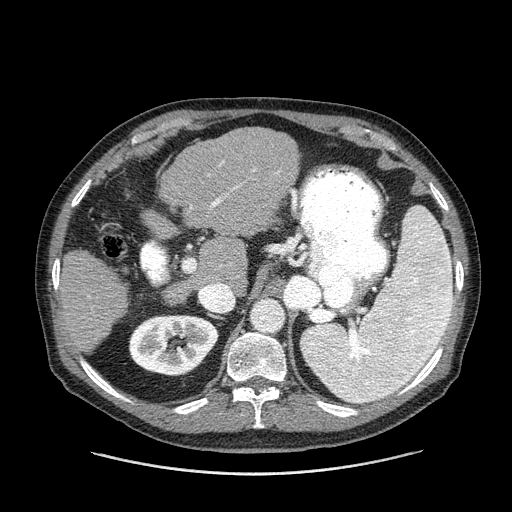
Contrast-enhanced abdominal CT (liver protocol), one axial slice; position 84 of 180 along the scan axis; reconstruction kernel STANDARD; 120 kVp; one of 2 acquisitions stored at this slice position; soft-tissue window (W 400 / L 40 HU); 2.5 mm slice thickness; 512 × 512 image matrix. From the clinical record (not read from this slice): diagnosis: hepatocellular carcinoma (patient treated with transarterial chemoembolisation; whether this scan precedes or follows treatment is not stated here); TNM stage (as recorded): Stage-II; Child-Pugh class: A; tumour nodularity: multinodular; tumour size: 2.8 cm.
Outlined on this slice (semi-automatically segmented with operator editing):
- liver parenchyma outside the tumour (the mass and vessels are separate outlines, so this box may not span the whole liver): bounding box <56,128,298,352> (left, top, right, bottom; pixels)
- liver vessels: <56,161,279,286>